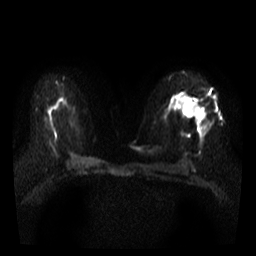
Breast MRI, one axial slice; position 21 of 36 along the scan axis; diffusion-weighted series; image 2 of 4 stored at this slice position (different b-values; order by instance number); 3 T; 5 mm slice thickness; 256 × 256 image matrix, field of view 300 × 300 mm. Female patient.
Annotated regions visible in this slice (manually delineated by an expert):
- tumour on diffusion-weighted imaging: bounding box [x1, y1, x2, y2] px = [181, 104, 204, 122]